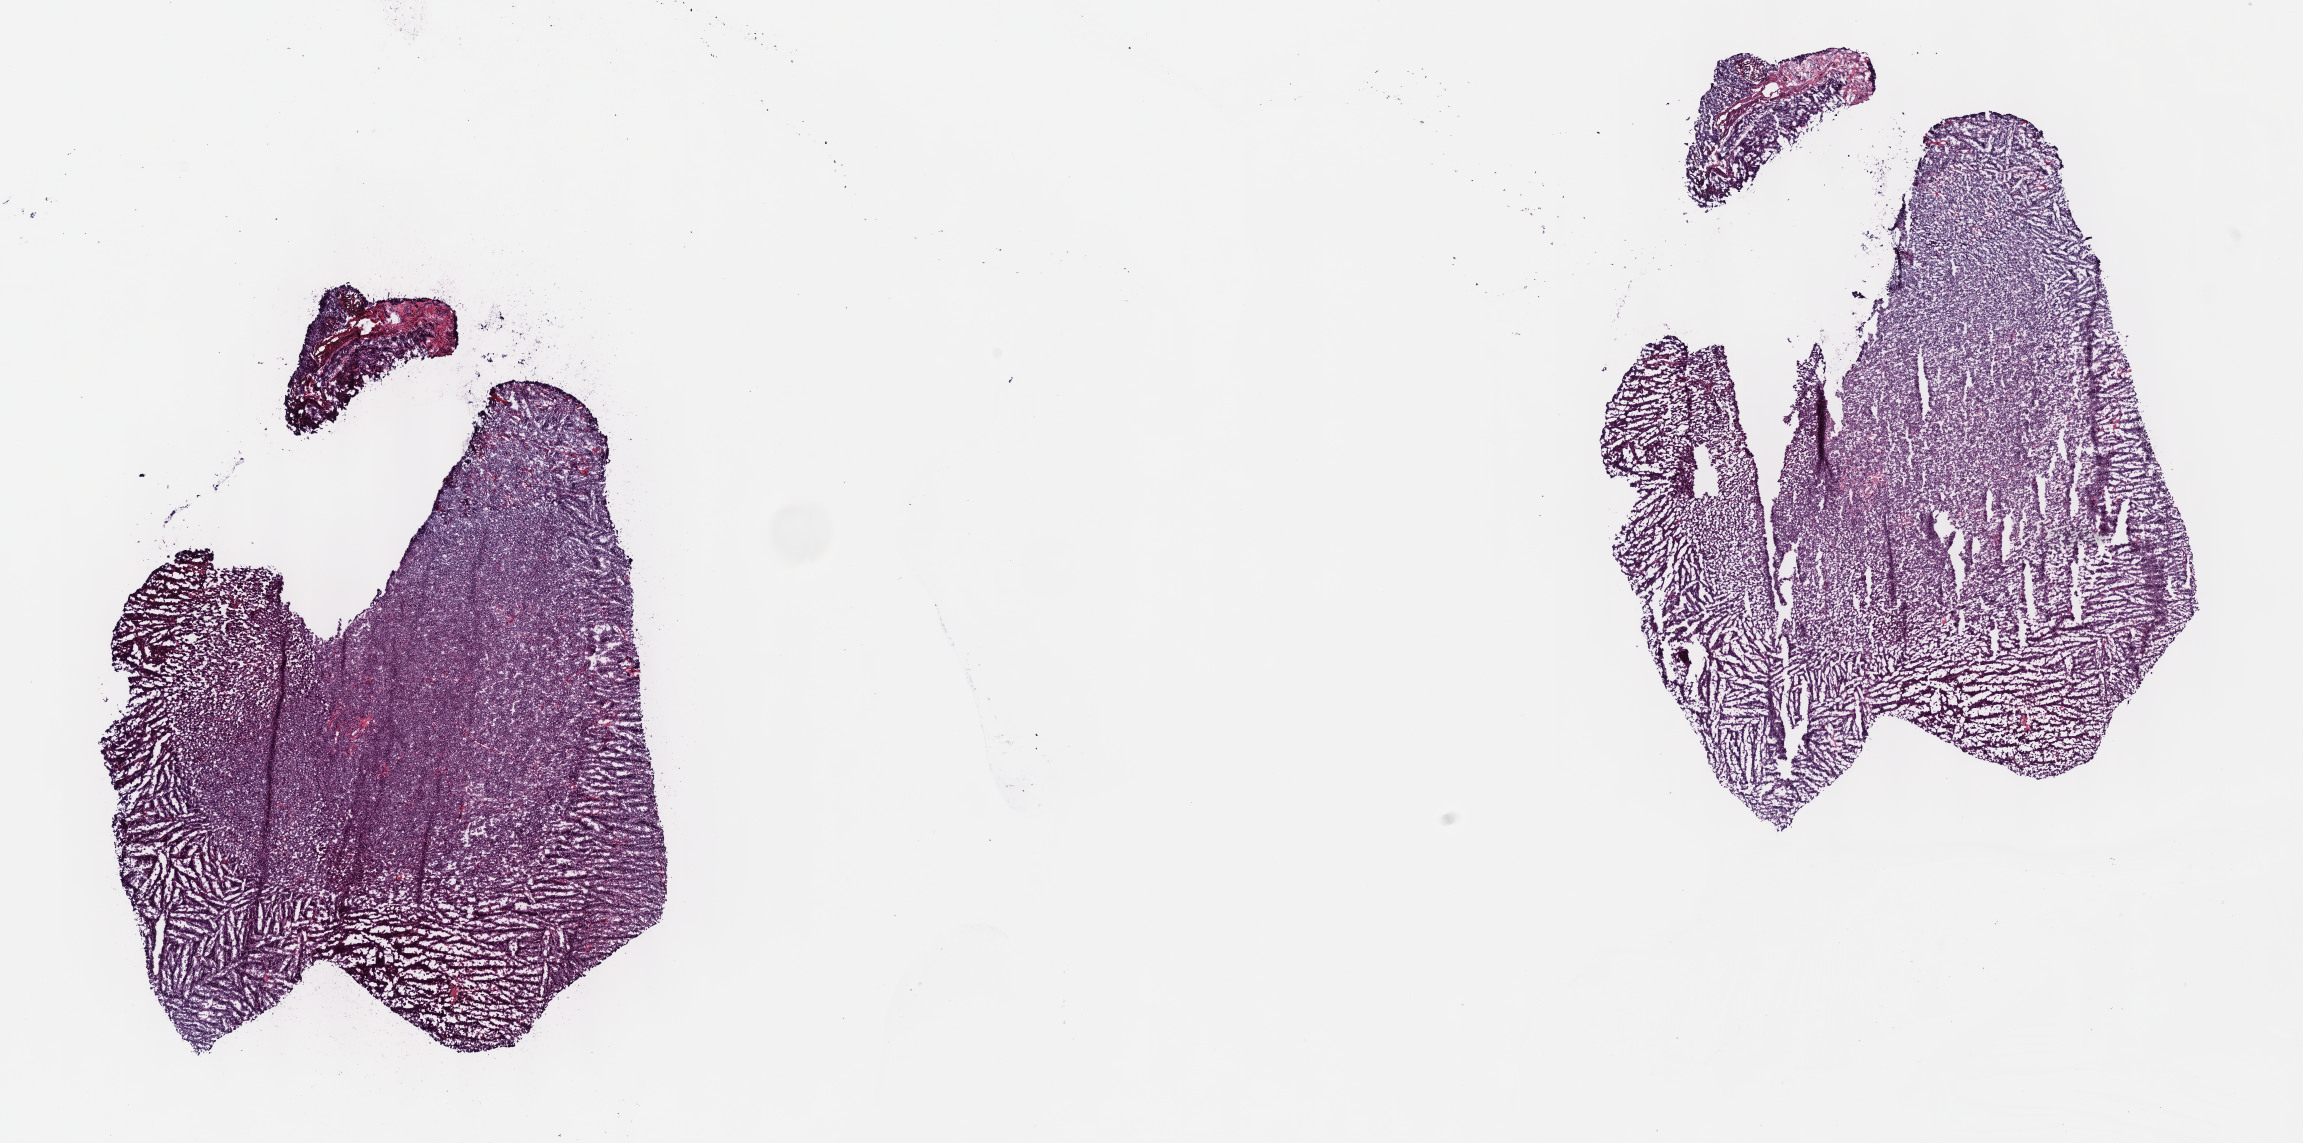
H&E whole-slide image, low-resolution overview of the scanned area, about 18.6 x 9.2 mm, frozen section from the top of the tissue portion, sample: primary tumour, lymphoid tissue. Male, age 46 years at initial diagnosis. Slide review estimates, as recorded: tumour cells 85%, tumour nuclei 90%, normal cells 5%, stromal cells 5%, necrosis 5%. Inflammatory infiltration, as recorded: lymphocyte infiltration 85%, monocyte infiltration 5%, neutrophil infiltration 5%.
Diagnosis: Diffuse large B-cell lymphoma, NOS (connective, subcutaneous and other soft tissues of head, face, and neck).